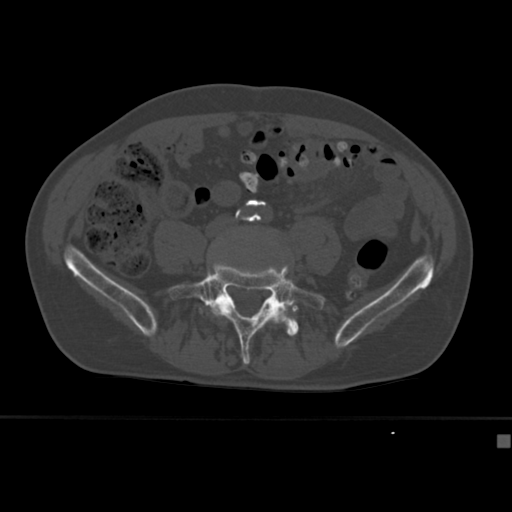
CT including the spine, one axial slice. Position 91 of 430 along the scan axis. Reconstruction kernel Br40s. 120 kVp. Bone window (W 1800 / L 400 HU). 1.5 mm slice thickness. 512 × 512 image matrix. Patient: male, 64 years. From the clinical record (not read from this slice): primary cancer: uterus.
Annotated regions visible in this slice (semi-automatic segmentation, software-assisted and operator-edited):
- L4 vertebra: bounding box <210,230,289,318> (left, top, right, bottom; pixels)
- L5 vertebra: <169,261,326,365>